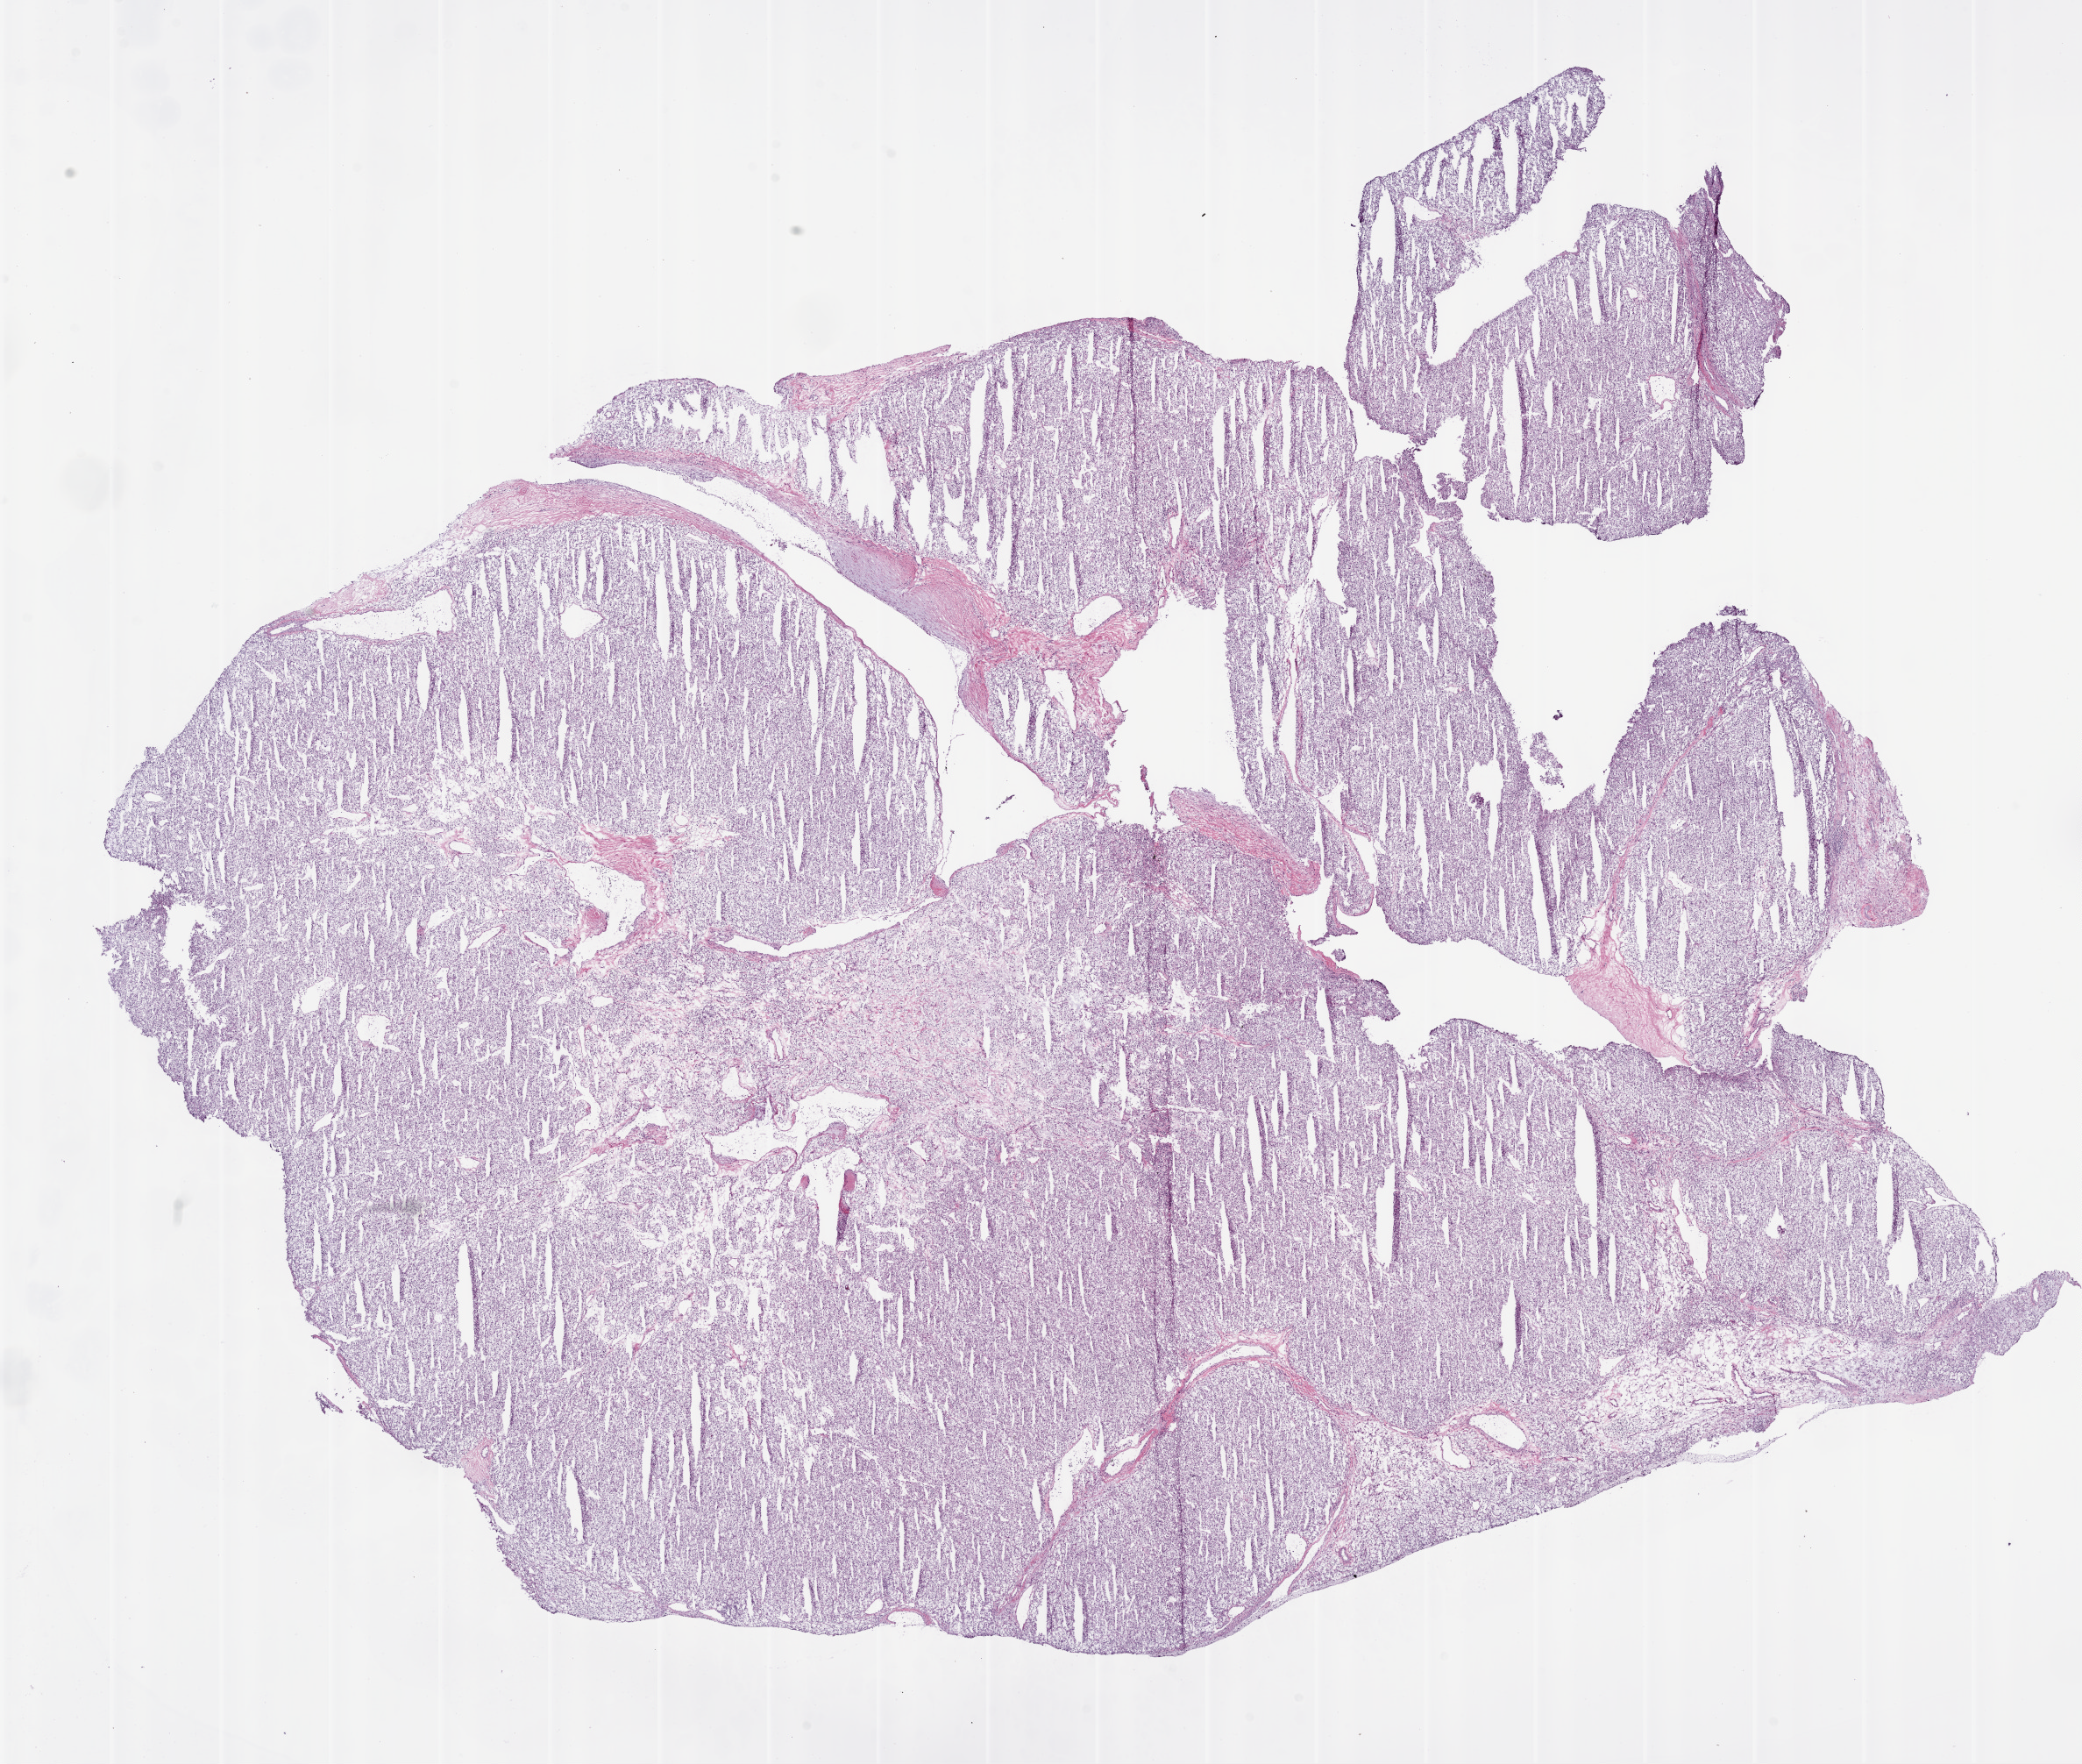
Hematoxylin and eosin (H&E) stained whole-slide image — whole scanned area (about 19.1 x 16.1 mm, acquisition: 20x scan) shown as a low-resolution overview, frozen section from the bottom of the tissue portion, primary tumour sample from the kidney. Patient: female, age at initial diagnosis 58 years. Histologic grade: G2 (moderately differentiated). Composition of this section per pathologist review: tumour cells 90%, tumour nuclei 90%, normal cells 5%, stromal cells 5%, necrosis 0%.
• diagnosis: Clear cell adenocarcinoma, NOS
• laterality: left
• AJCC pathologic stage: I